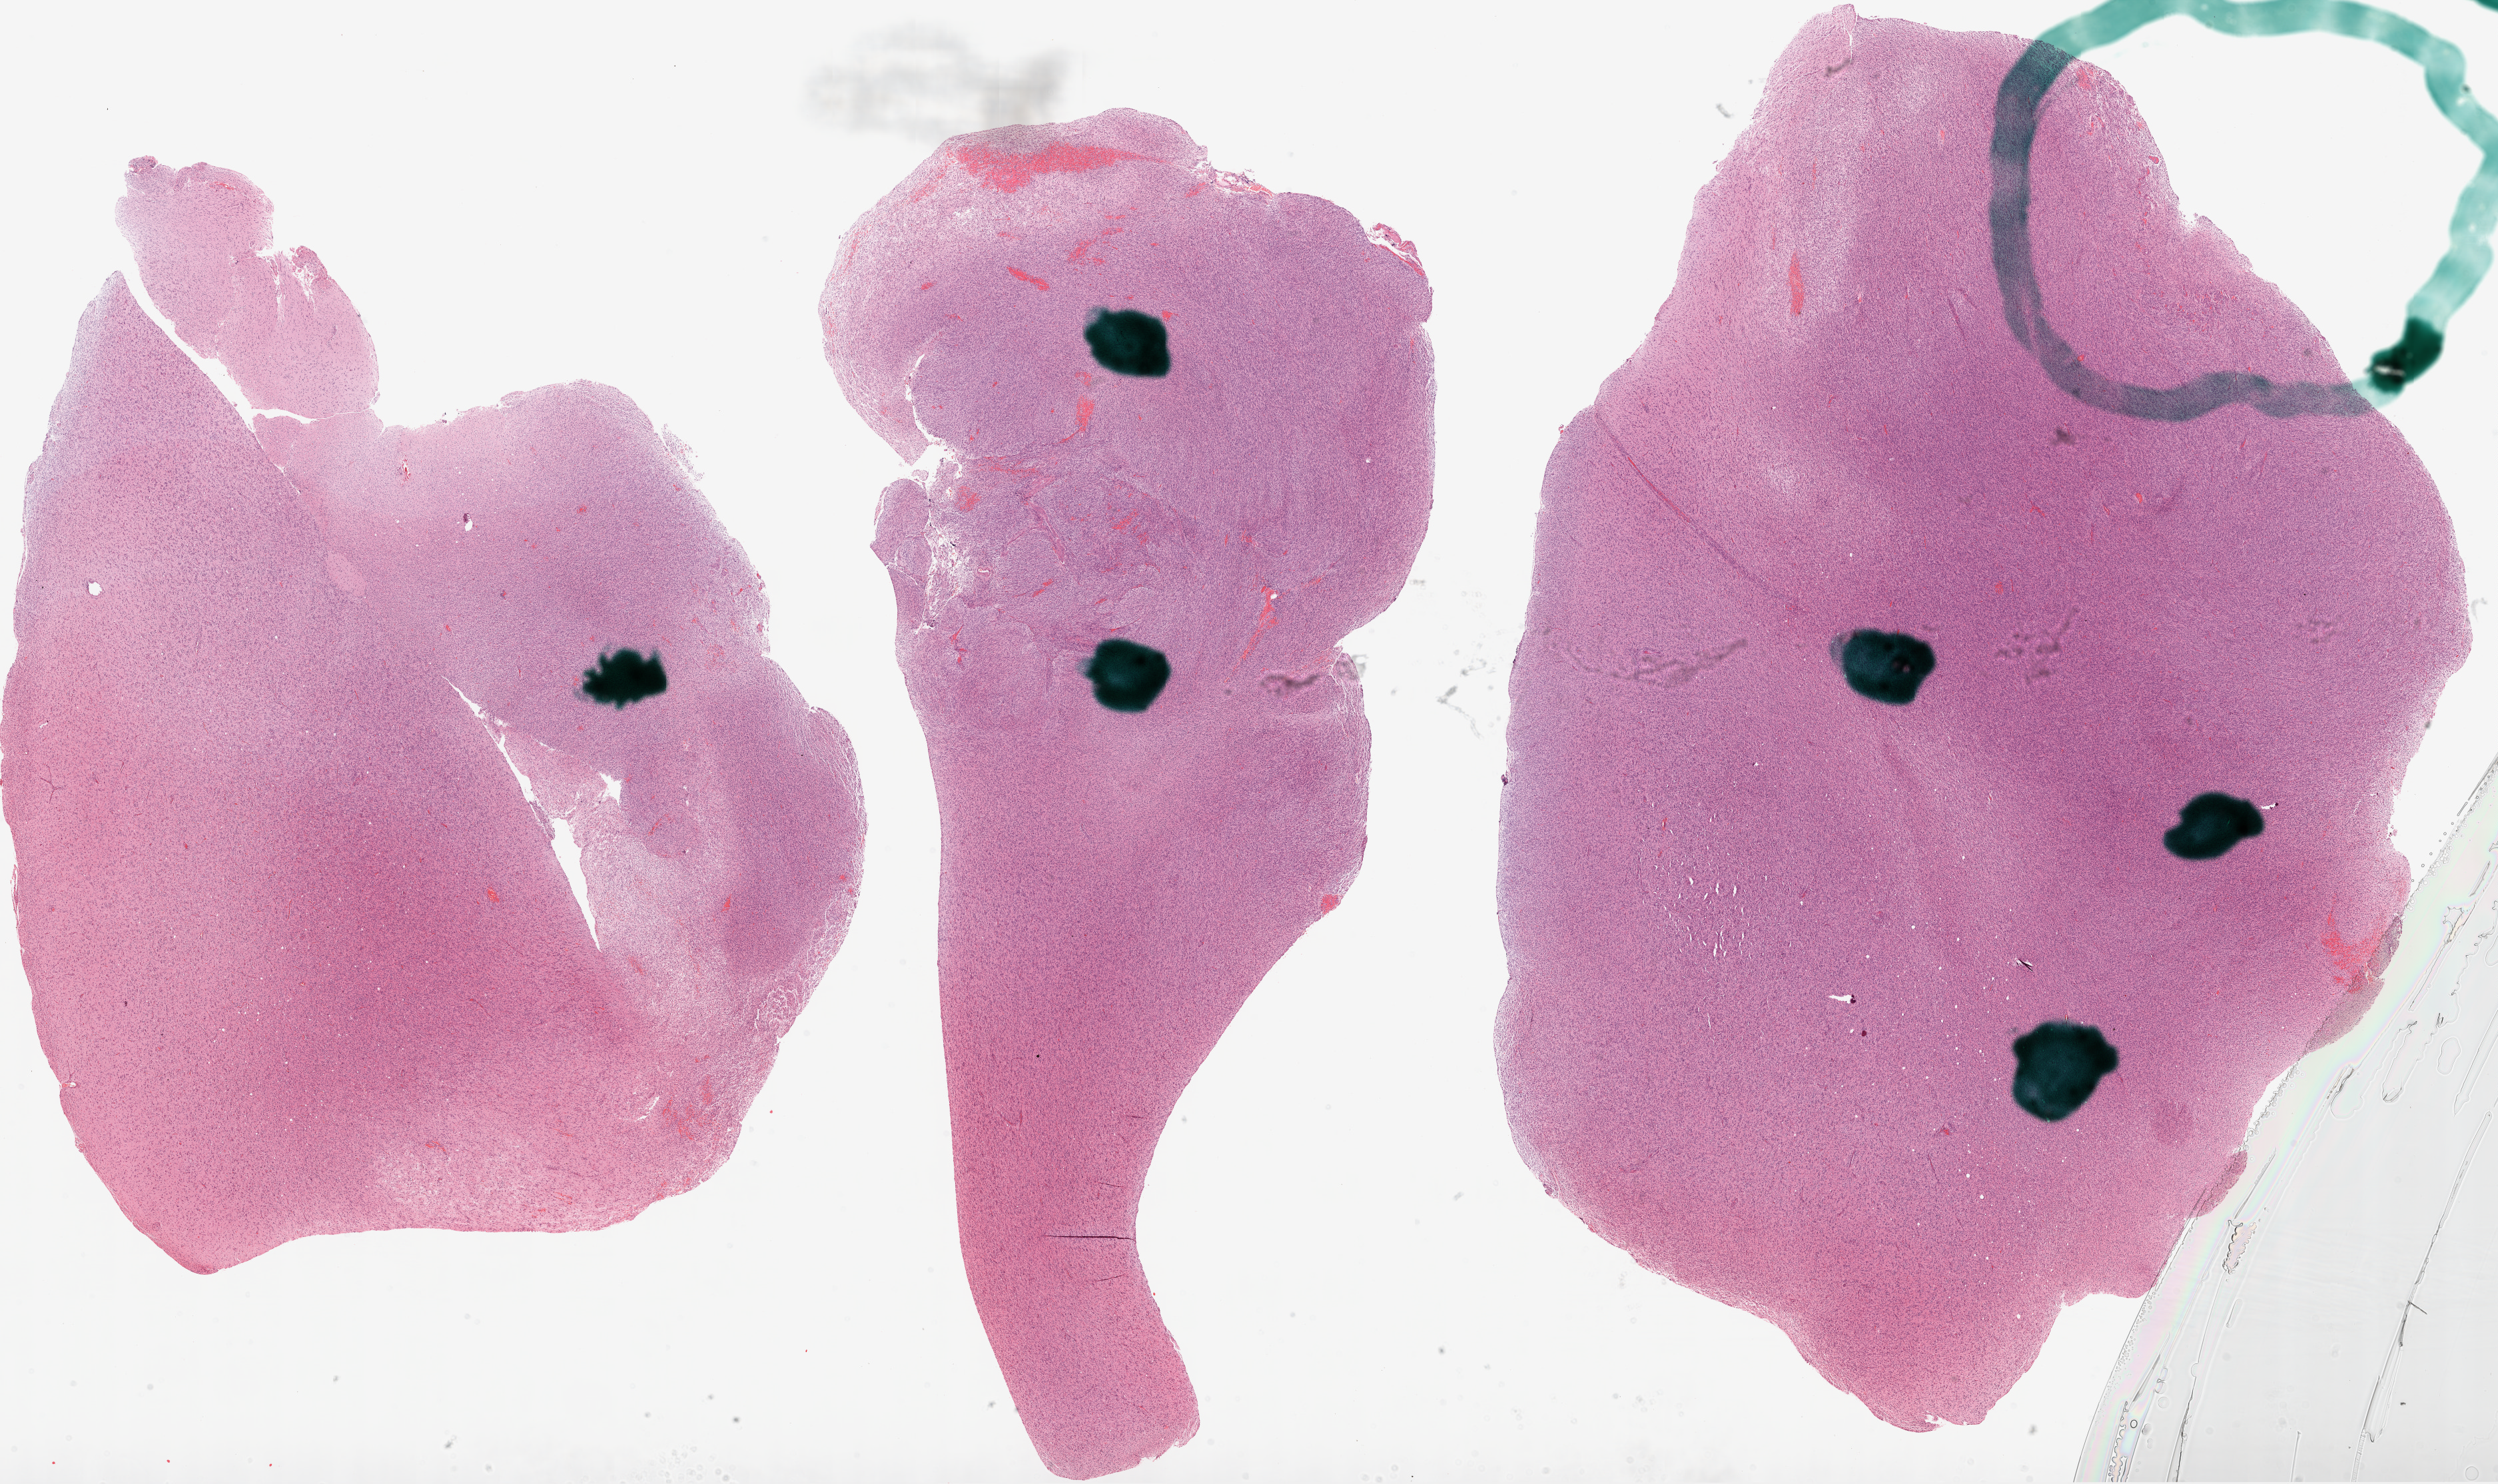
Digitized H&E-stained tissue section (whole slide), whole scanned area (about 30.1 x 17.9 mm, acquisition: 20x scan) shown as a low-resolution overview, formalin-fixed paraffin-embedded (FFPE) diagnostic section, primary tumour sample from the brain. Female patient; age at initial diagnosis 61 years.
Diagnosis: Glioblastoma.